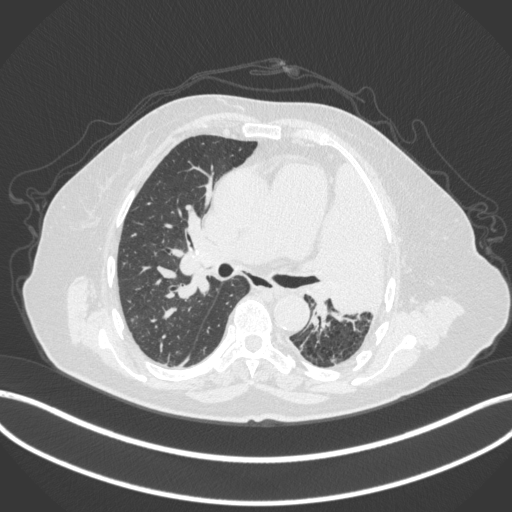
Chest CT, one axial slice. Reconstruction kernel B31f. Lung window (W 1500 / L -600 HU). 1 mm slice thickness. 512 × 512 image matrix, field of view 400 × 400 mm. Patient: female, 75 years. From the clinical record (not read from this slice): clinical TNM (as recorded): T3 N3 M1.
Structures marked on this image (bounding box drawn by a radiologist):
- lung tumour (recorded histology: adenocarcinoma): bounding box <318,144,383,320> (left, top, right, bottom; pixels)